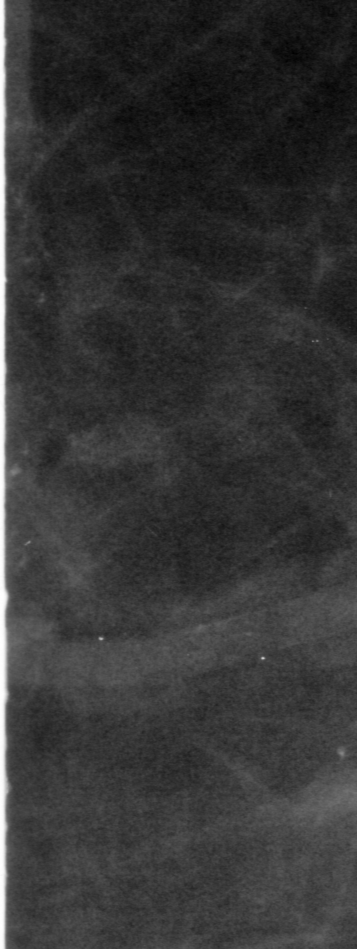
Cropped region of a digitized screen-film mammogram centred on a radiologist-marked abnormality; left breast; CC view.
Calcifications, morphology amorphous, distribution linear; BI-RADS assessment category 3; subtlety rating 2 on a 1 (subtle) to 5 (obvious) scale; pathology result (as recorded, not read from the image): malignant.